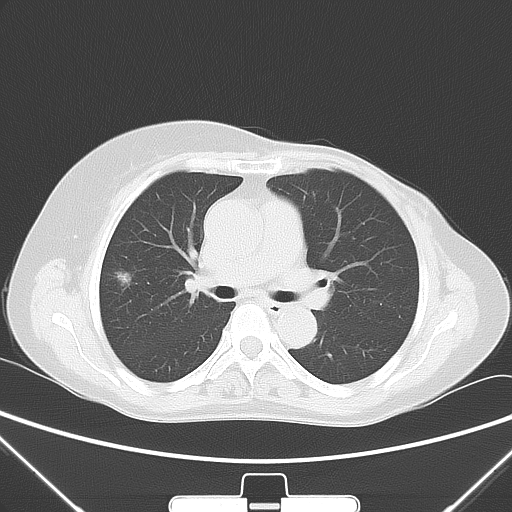
Chest CT, one axial slice. Slice 31 of 53 in the series (ordered by position). 120 kVp. Lung window (W 1500 / L -600 HU). 5 mm slice thickness. 512 × 512 image matrix, field of view 350 × 350 mm. Patient: female, 64 years. Case-level facts recorded for this patient, not image findings: clinical TNM (as recorded): T1c N0 M0; histopathological grade: G1-2.
Annotated regions visible in this slice (bounding box drawn by a radiologist):
- lung tumour (recorded histology: adenocarcinoma): box from (x=106, y=262) to (x=137, y=292) px